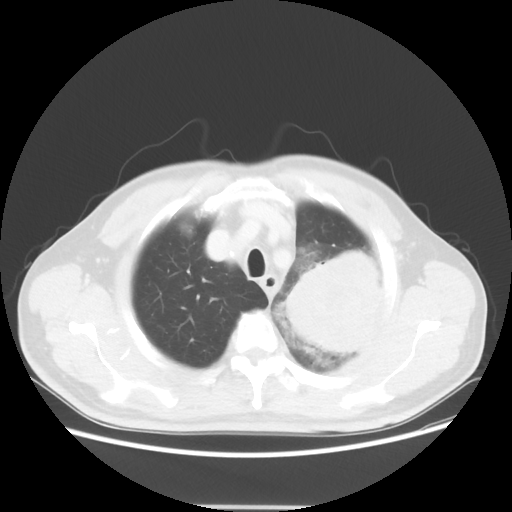
Chest CT, one axial slice. Slice 46 of 53 in the series (ordered by position). 100 kVp. Lung window (W 1500 / L -600 HU). 5 mm slice thickness. 512 × 512 image matrix. Patient: male, 60 years. From the clinical record (not read from this slice): clinical TNM (as recorded): T4 N1 M1a; histopathological grade: G3.
Structures marked on this image (rectangle marked by the reading radiologist):
- lung tumour (recorded histology: large cell carcinoma): bounding box [x1, y1, x2, y2] px = [272, 244, 396, 364]